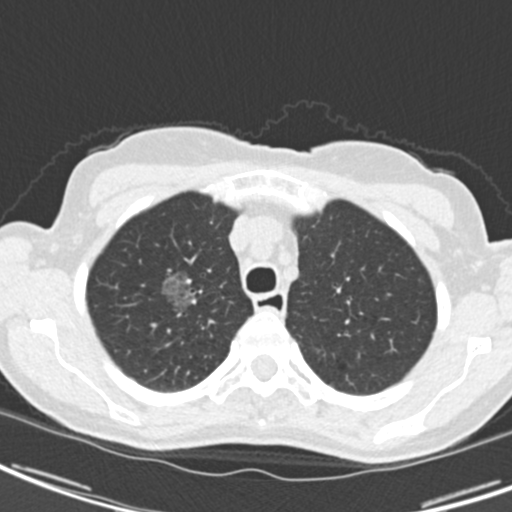
Low-dose screening chest CT, one axial slice. Position 159 of 189 along the scan axis. Reconstruction kernel B30f. Lung window (W 1500 / L -600 HU). 2 mm slice thickness. 512 × 512 image matrix.
Annotated regions visible in this slice (outlined manually by an expert reader):
- lesion 1 (tumor, upper lobe of right lung): bounding box (x1, y1, x2, y2) in pixels: (162, 271, 192, 310)